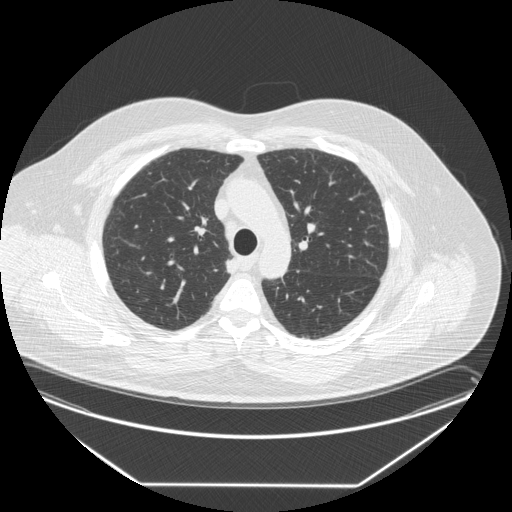
Low-dose screening chest CT, one axial slice; slice 195 of 258 in the series (ordered by position); lung window (W 1500 / L -600 HU); 2.5 mm slice thickness; 512 × 512 image matrix, field of view 440 × 440 mm.
Structures marked on this image (manually delineated by an expert):
- lesion 1 (tumor, upper lobe of right lung): box from (x=226, y=256) to (x=239, y=274) px